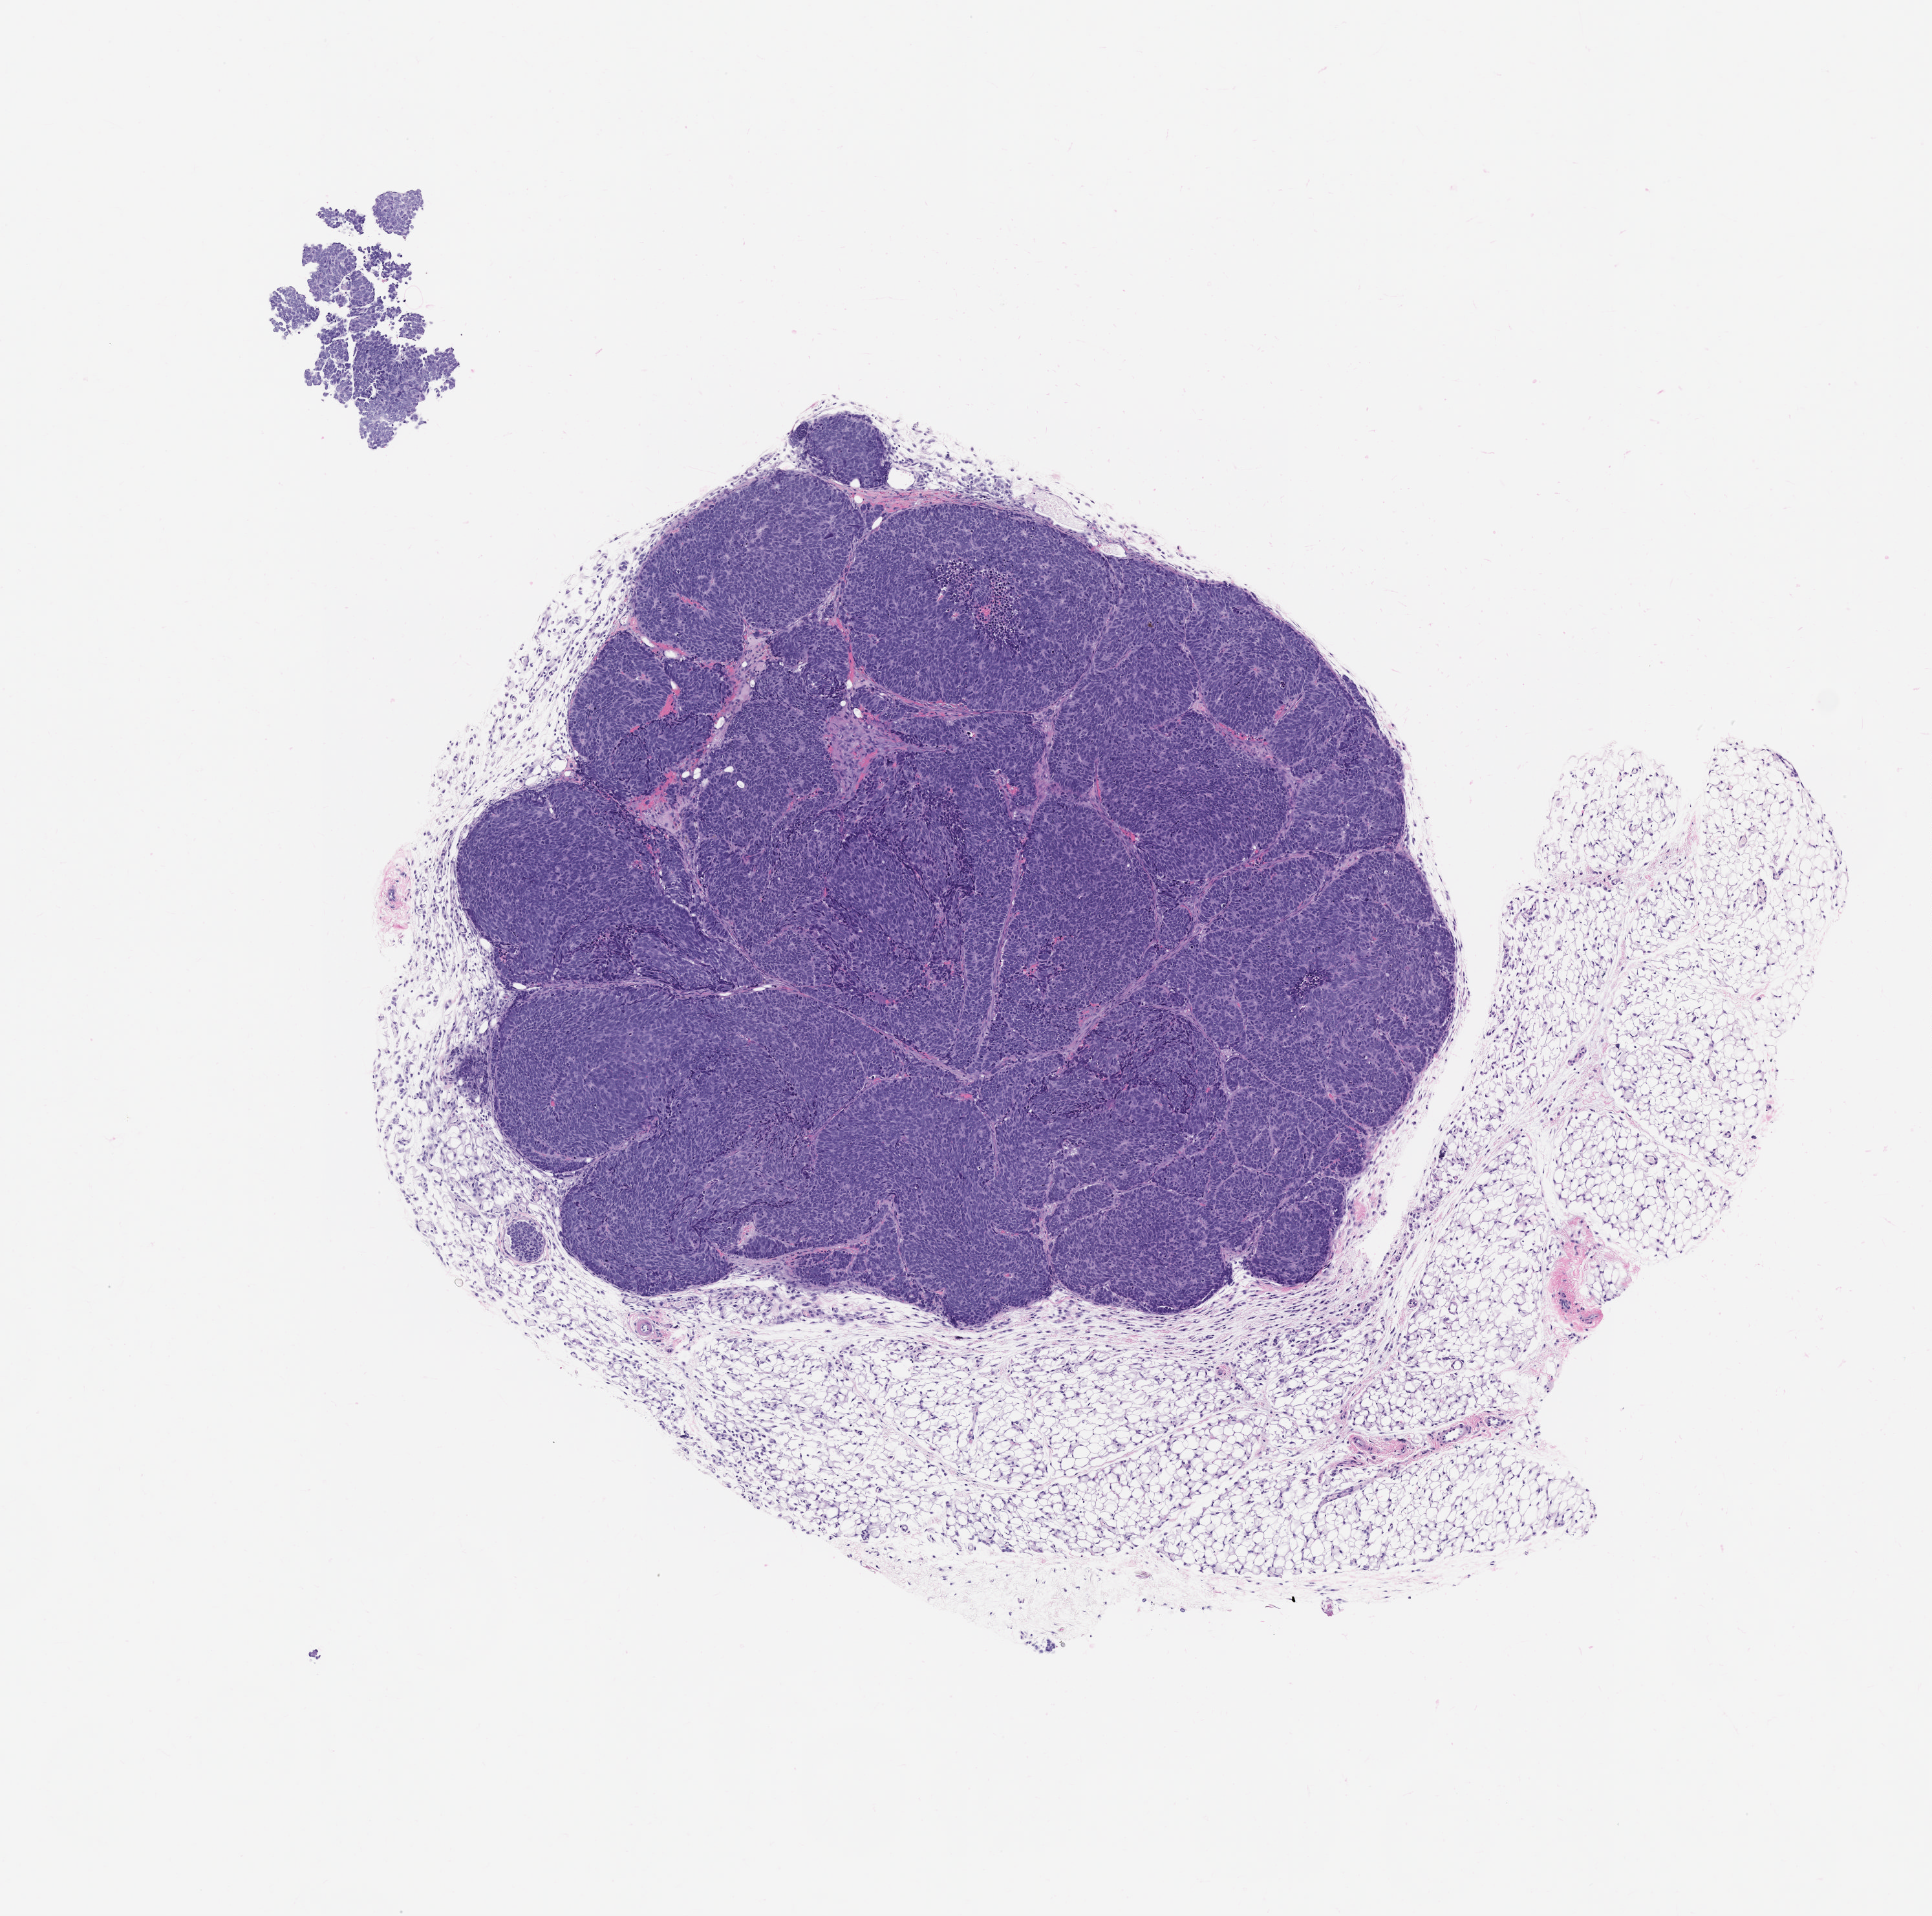
Haematoxylin and eosin whole-slide image of a patient-derived xenograft (PDX) tumor grown in a mouse, passage 1, shown as a low-resolution overview of the whole scanned area (about 6.0 x 6.0 mm); formalin-fixed, paraffin-embedded (FFPE) tissue; tumor site category: bladder.
Originating patient diagnosis: Bladder Small Cell Neuroendocrine Carcinoma.